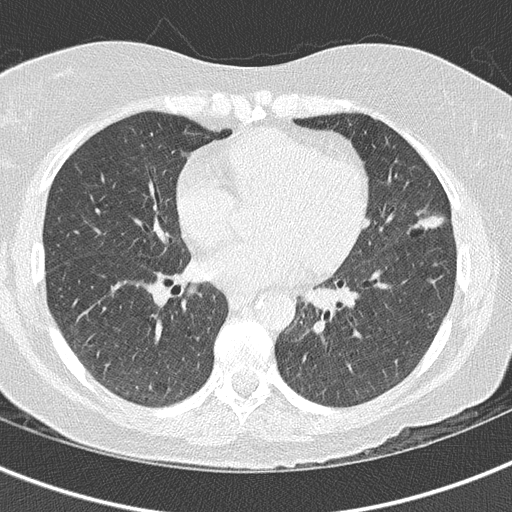
Low-dose screening chest CT, axial slice; third annual screen; lung window (W 1500 / L -600 HU); 2 mm slice thickness. Female, age 63 years at enrolment.
Expert reader's lesion annotation, bounding box <390,197,457,250> (left, top, right, bottom; pixels). The screening reader recorded 5 non-calcified nodules or masses ≥4 mm on this exam (lingula, left lower lobe, right upper lobe, right upper lobe, right upper lobe); which of them this box marks is not recorded. Official screen result: positive, other. Lung cancer was diagnosed 35 days after this screen: bronchiolo-alveolar adenocarcinoma, NOS, lingula, stage IA (AJCC 6th edition), 14 mm at pathology.